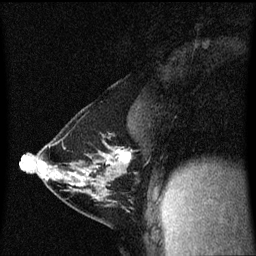
Breast MRI (dynamic contrast-enhanced), one sagittal slice; position 33 of 60 along the scan axis; dynamic contrast-enhanced series, image 2 of 3 at this slice position (ordered by acquisition); 1.5 T; TE 4.2 ms, TR 8.4 ms; 2 mm slice thickness; 256 × 256 image matrix. Patient: female, 40 years. Case-level facts recorded for this patient, not image findings: setting: breast cancer imaged before/during neoadjuvant chemotherapy; receptor status: triple-negative.
Outlined on this slice (semi-automatic segmentation, software-assisted and operator-edited):
- analysis volume of interest (the breast-tissue region the enhancement analysis was run in; not a lesion): bounding box <34,144,133,199> (left, top, right, bottom; pixels)
- tumour enhancement mask (voxels above the 70 % enhancement threshold inside the analysis volume of interest): <74,152,131,181>